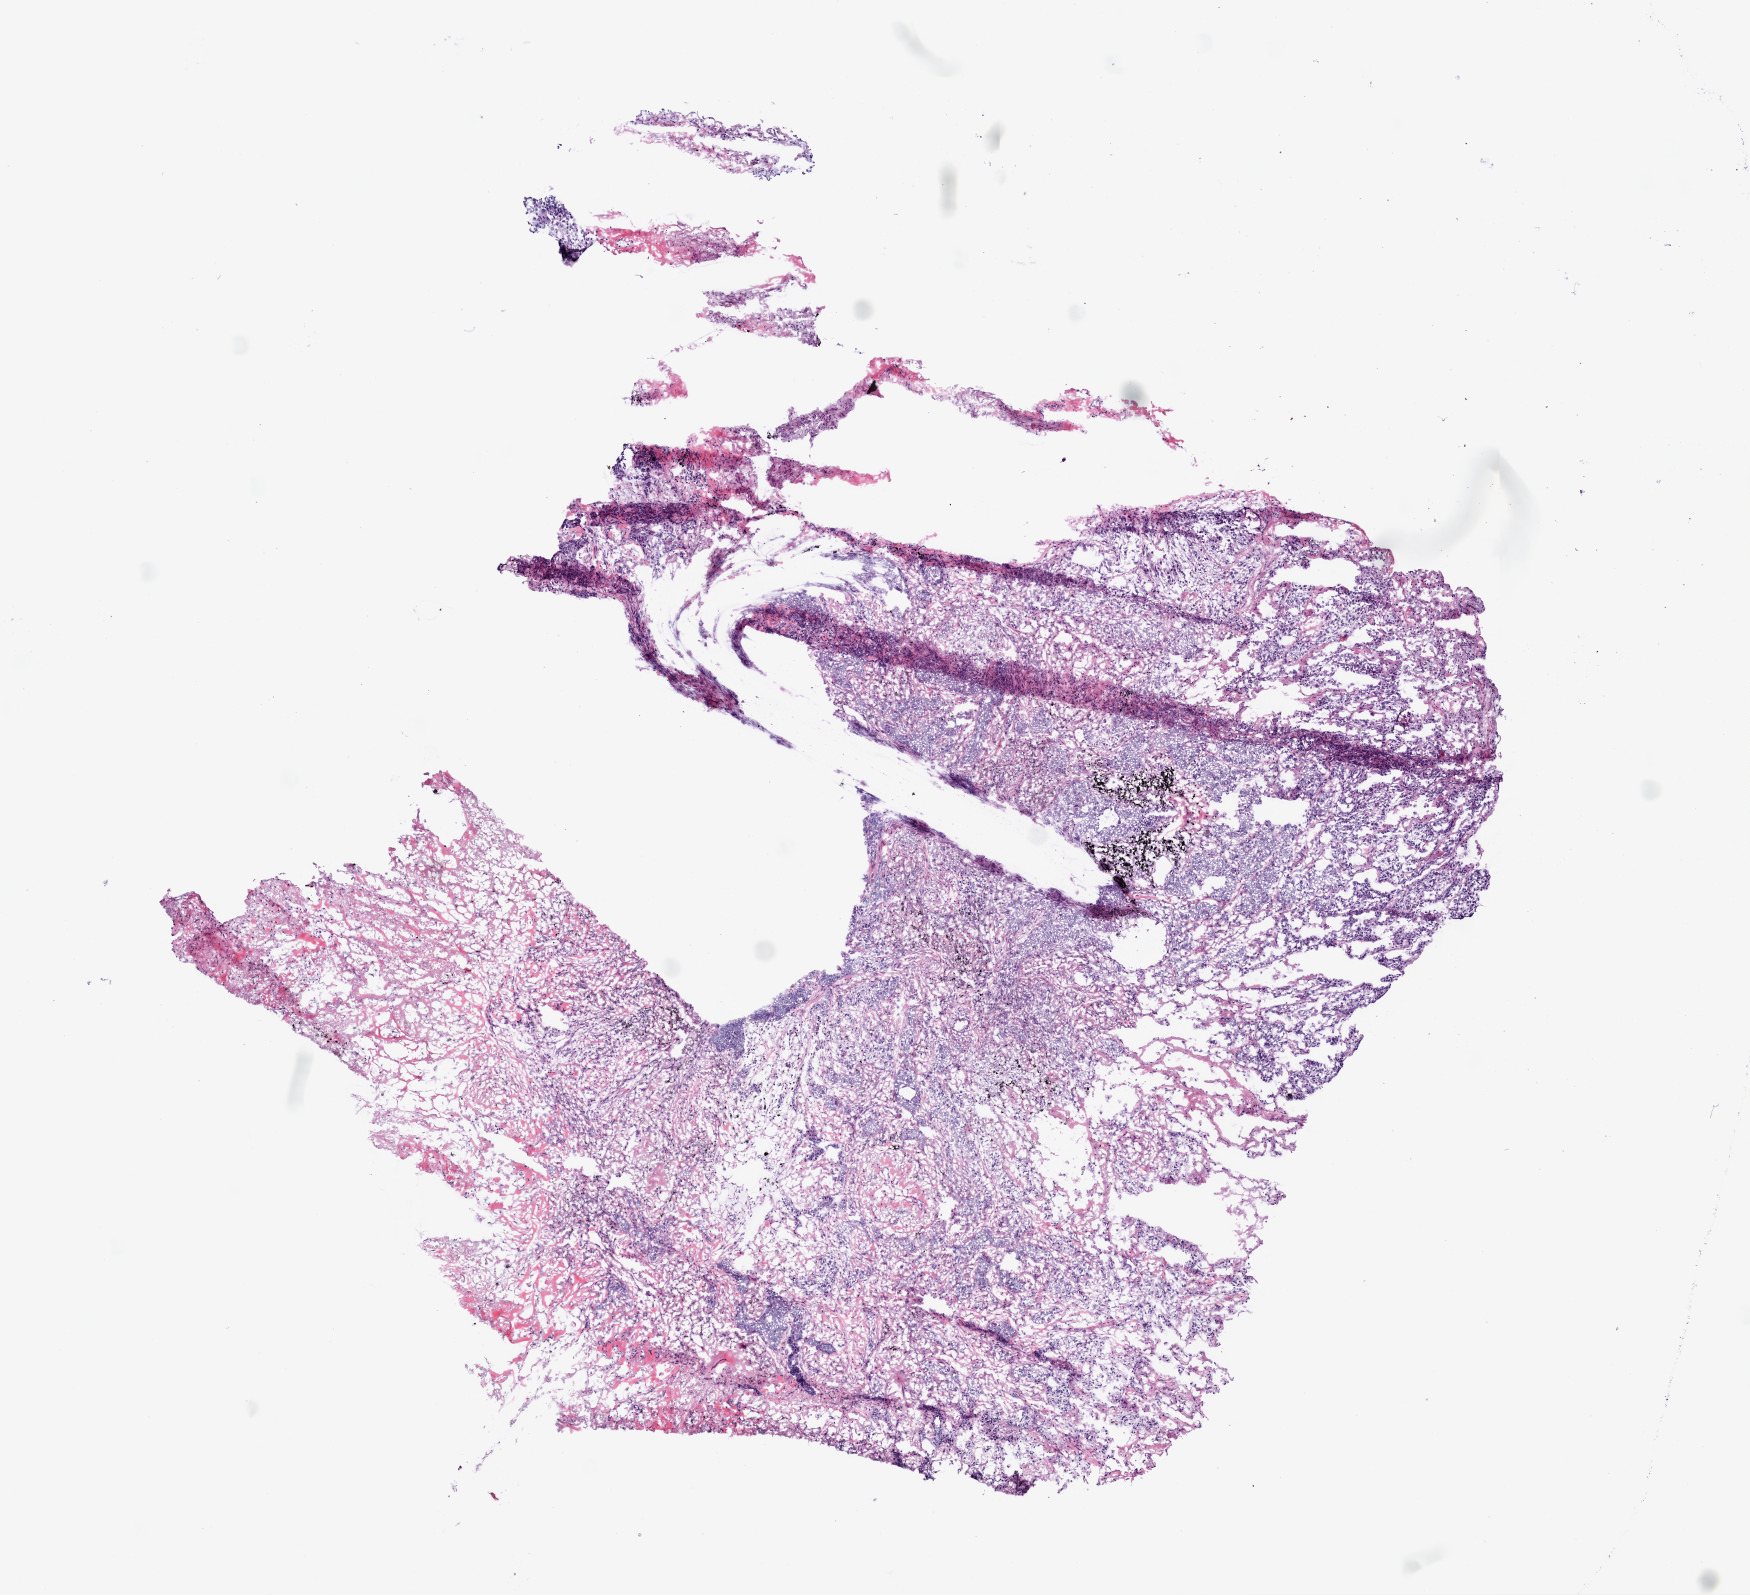
Whole-slide histology image, H&E, low-resolution overview of the scanned area, about 7.0 x 6.4 mm; frozen section; sample: primary tumour, lung. Patient: male, age at initial diagnosis 74 years. Composition of this section per pathologist review: tumour cells 60%, tumour nuclei 70%, normal cells 0%, stromal cells 20%, necrosis 20%.
Laterality: left. AJCC pathologic stage: IA (6th edition). Pathologic diagnosis: Basaloid squamous cell carcinoma (upper lobe, lung).